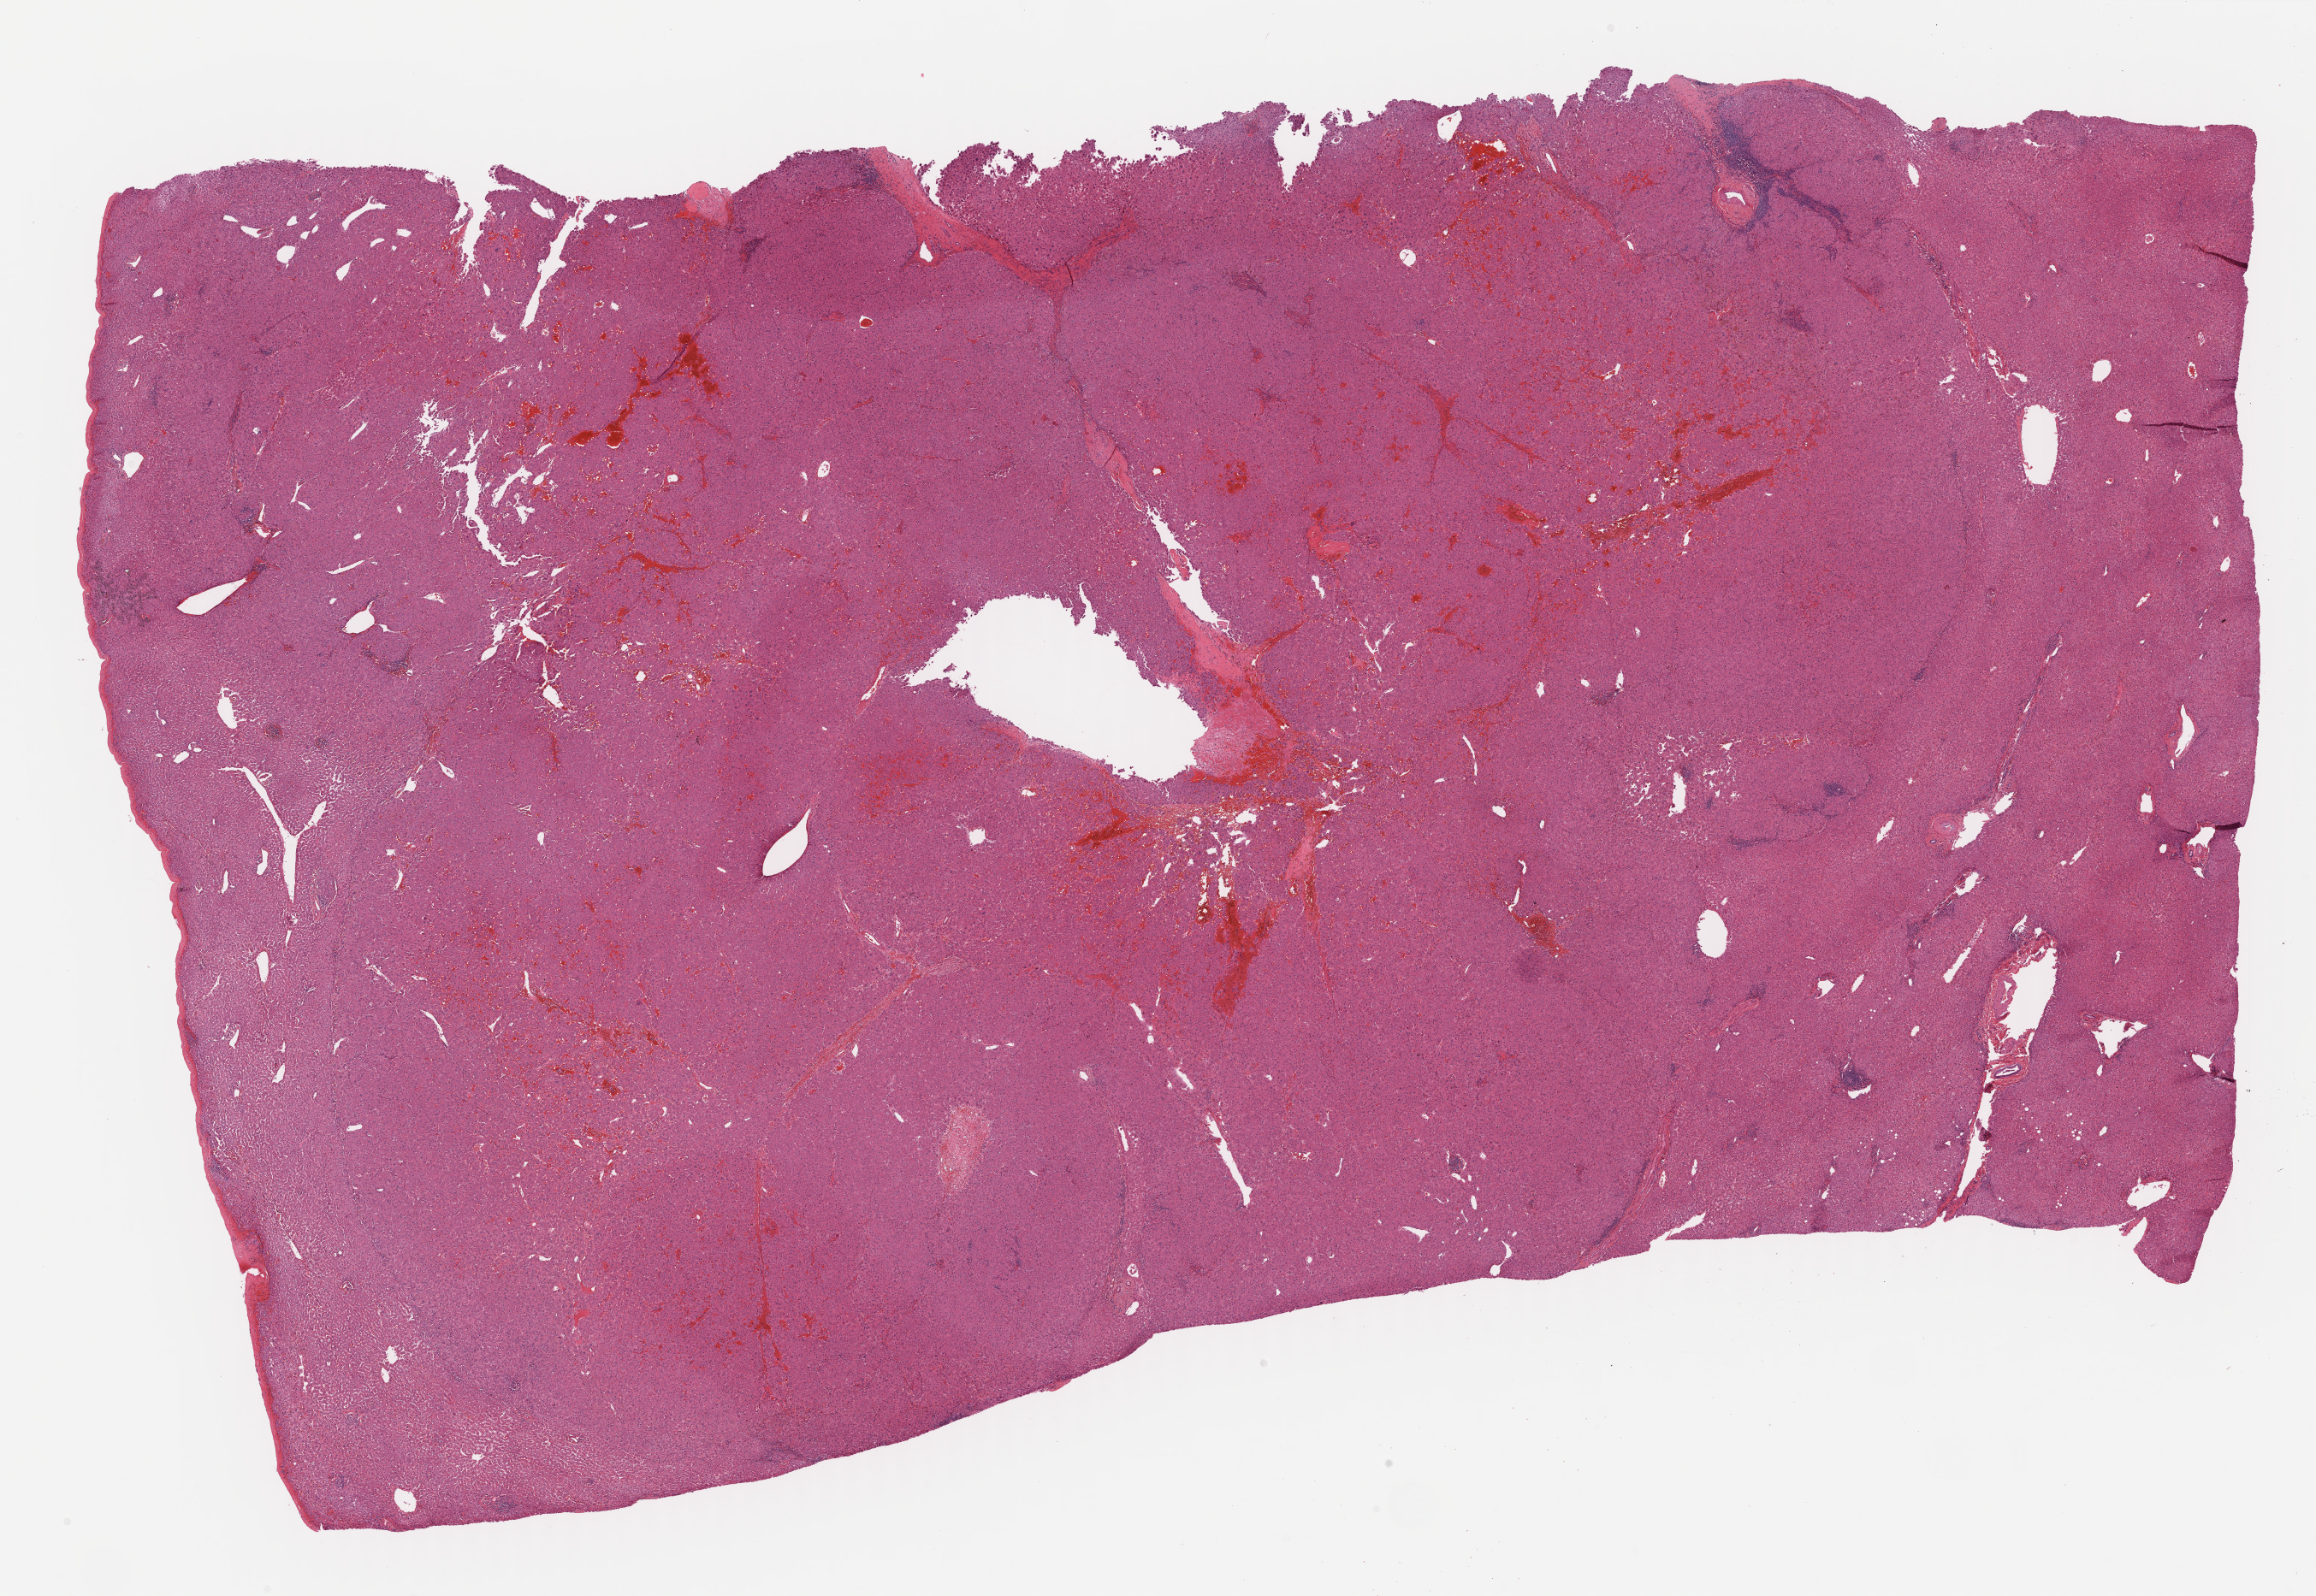
Whole-slide histology image, H&E — low-resolution overview of the scanned area, about 21.9 x 15.1 mm, formalin-fixed paraffin-embedded (FFPE) diagnostic section, liver, primary tumour sample. Patient: male, age at initial diagnosis 68 years. Histologic grade: G1 (well differentiated).
TNM: T1 N0 M0. Diagnosis: Hepatocellular carcinoma, NOS. AJCC pathologic stage: I (6th edition).